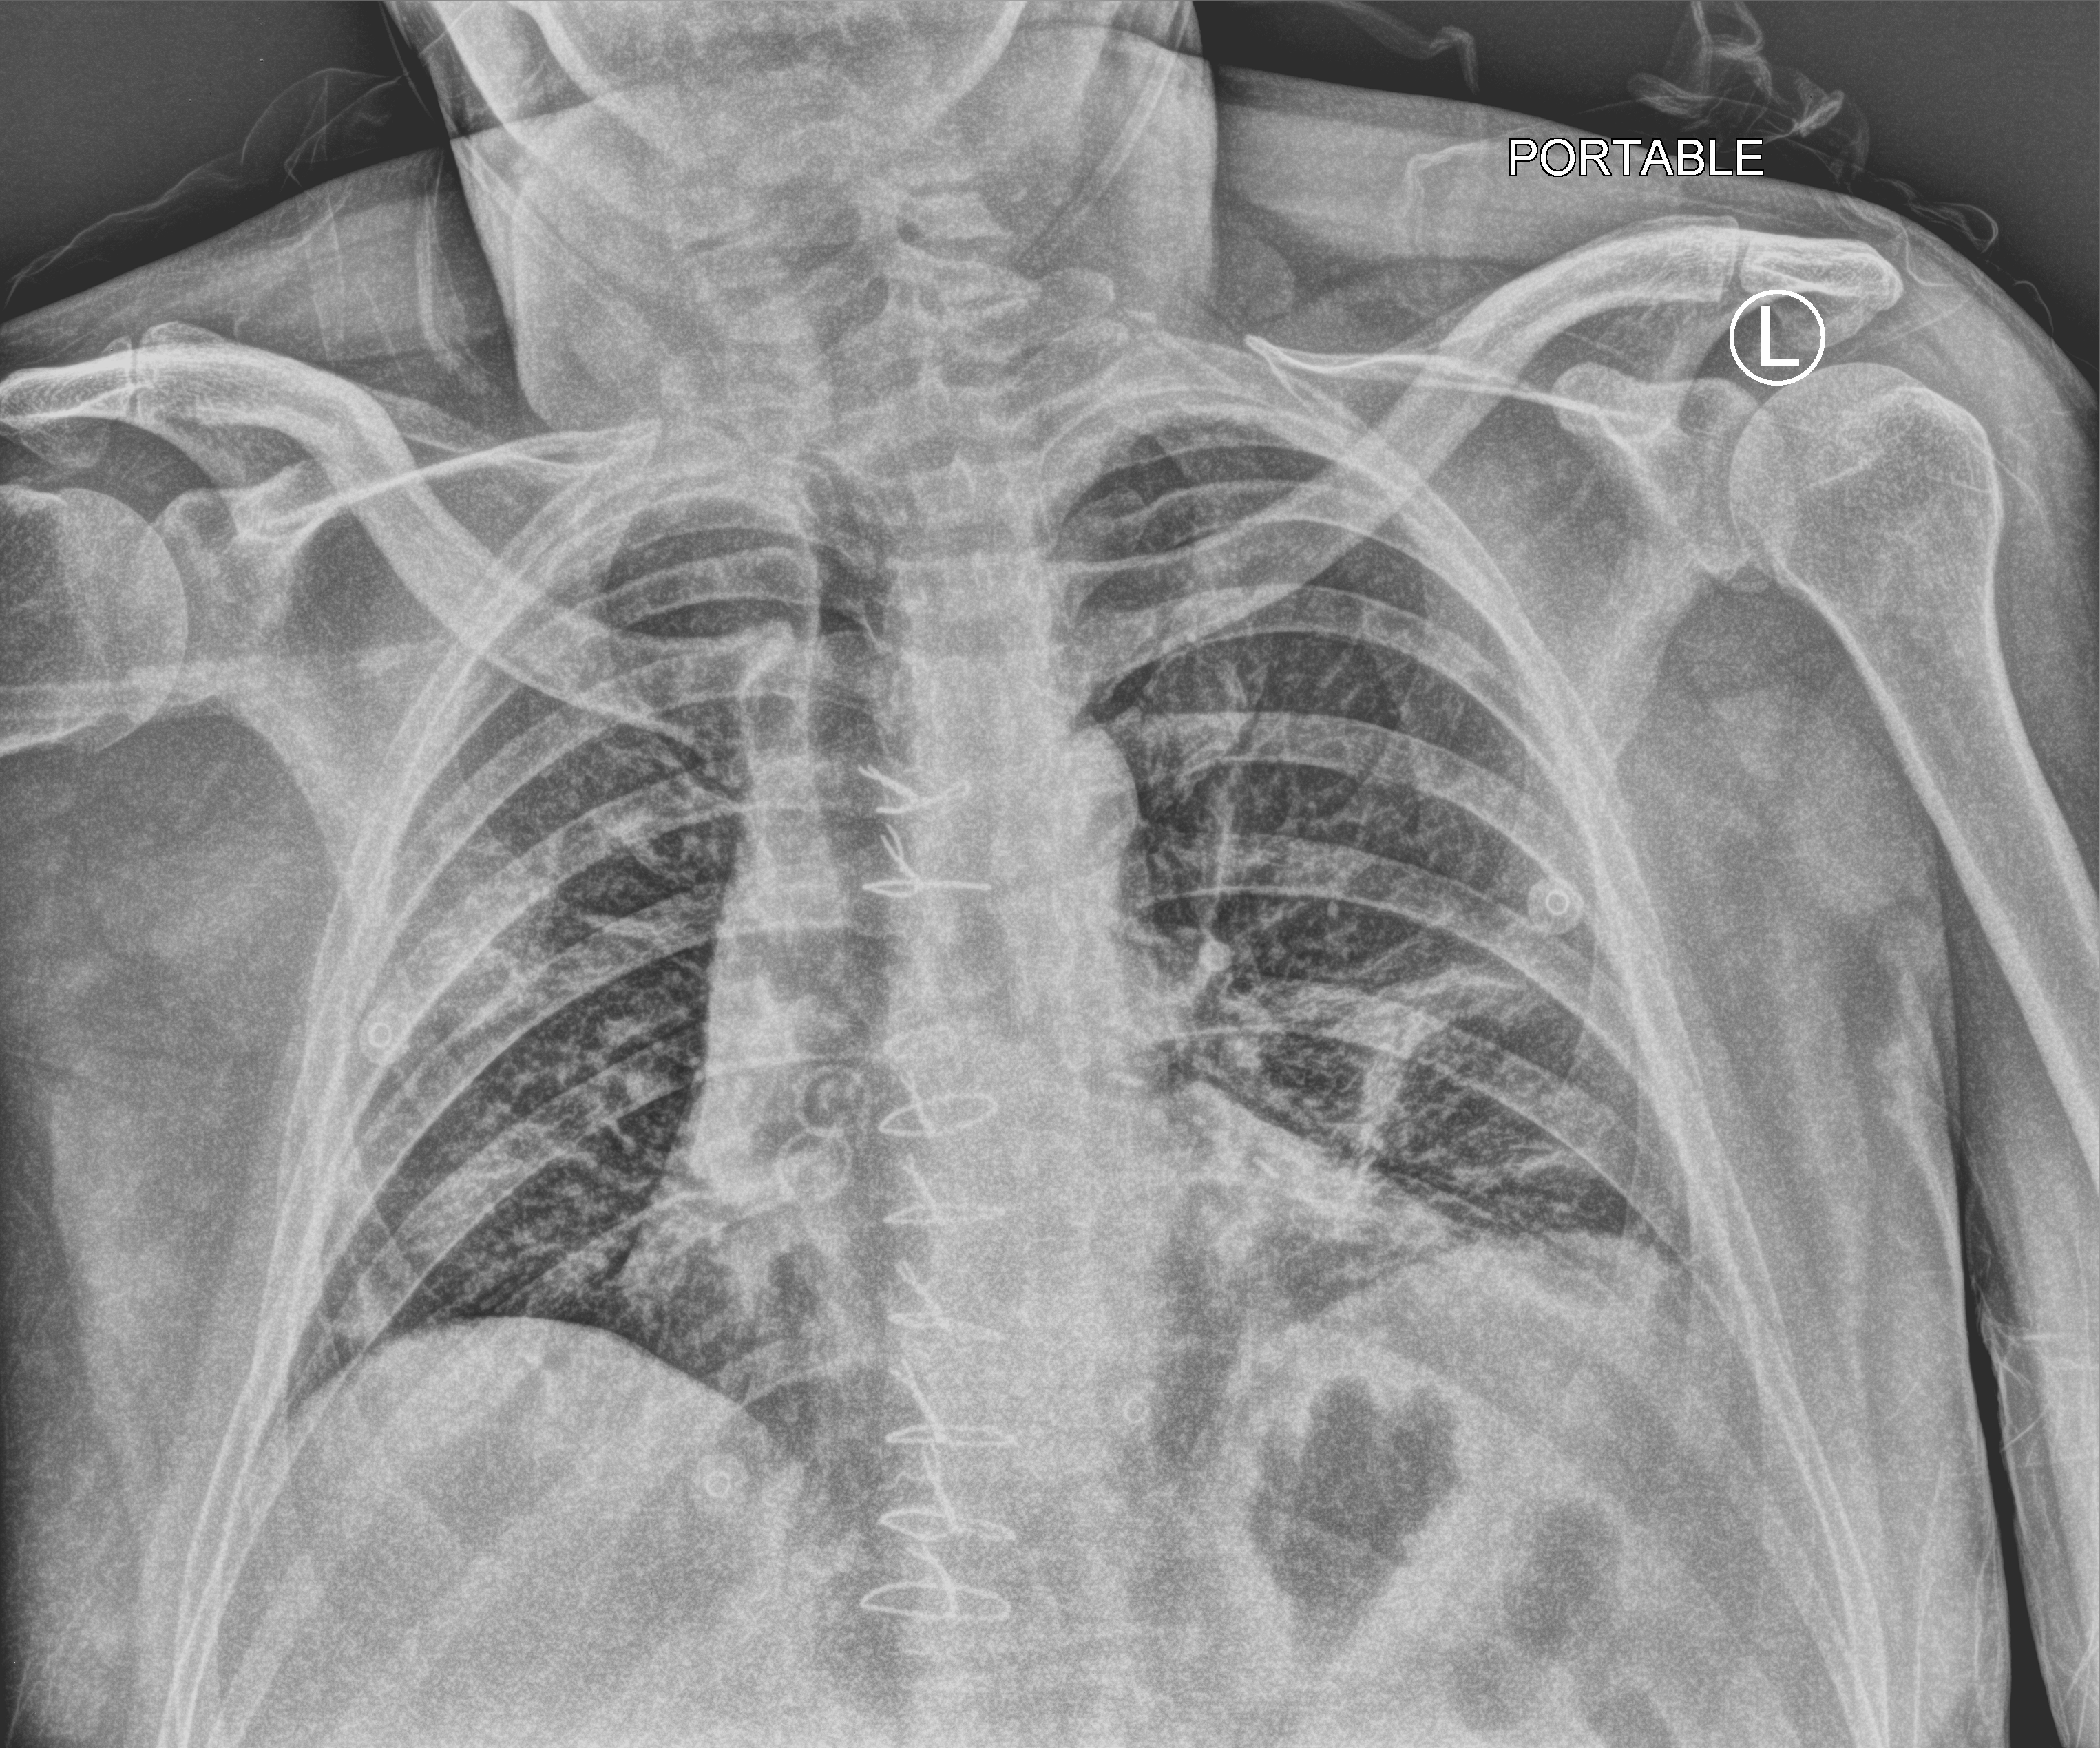
Chest X-ray (portable), anteroposterior (AP) projection. Male patient hospitalised with COVID-19, age 18–59 years.
Admission-level facts for this patient (not findings on this image; timing relative to this image not recorded):
- admitted to intensive care during this hospital stay: yes